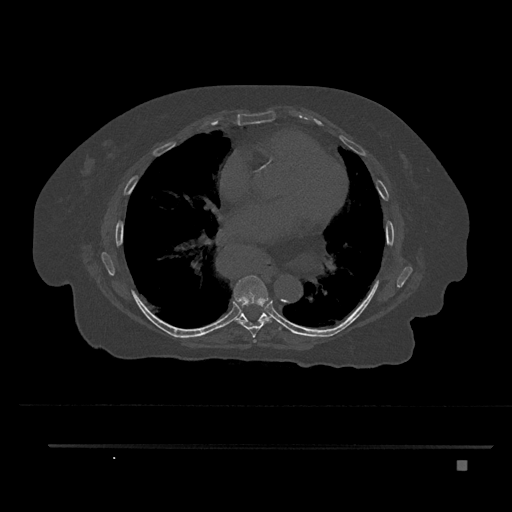
CT including the spine, one axial slice; slice 467 of 797 in the series (ordered by position); reconstruction kernel Br40s/3; 120 kVp; bone window (W 1800 / L 400 HU); 0.5 mm slice thickness; 512 × 512 image matrix. Female patient, age 76 years. Case-level facts recorded for this patient, not image findings: primary cancer: lung.
Outlined on this slice (semi-automatically segmented with operator editing):
- T6 vertebra: bounding box (x1, y1, x2, y2) in pixels: (253, 339, 257, 343)
- T7 vertebra: (233, 275, 272, 338)
- T8 vertebra: (237, 308, 282, 330)